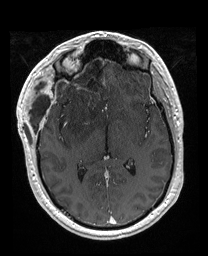
Brain MRI from a brain-tumour surgery series, one axial slice. Position 98 of 176 along the scan axis. T1-weighted post-contrast. 1 mm slice thickness. 208 × 256 image matrix, field of view 208 × 256 mm. Case-level facts recorded for this patient, not image findings: histopathology: Astrocytoma; WHO grade: 4; IDH mutation: yes; tumour location: Right Orbitofrontal Anterior Temporal Insular.
Annotated regions visible in this slice (outlined manually by an expert reader):
- previous resection cavity: bounding box (x1, y1, x2, y2) in pixels: (56, 52, 106, 84)